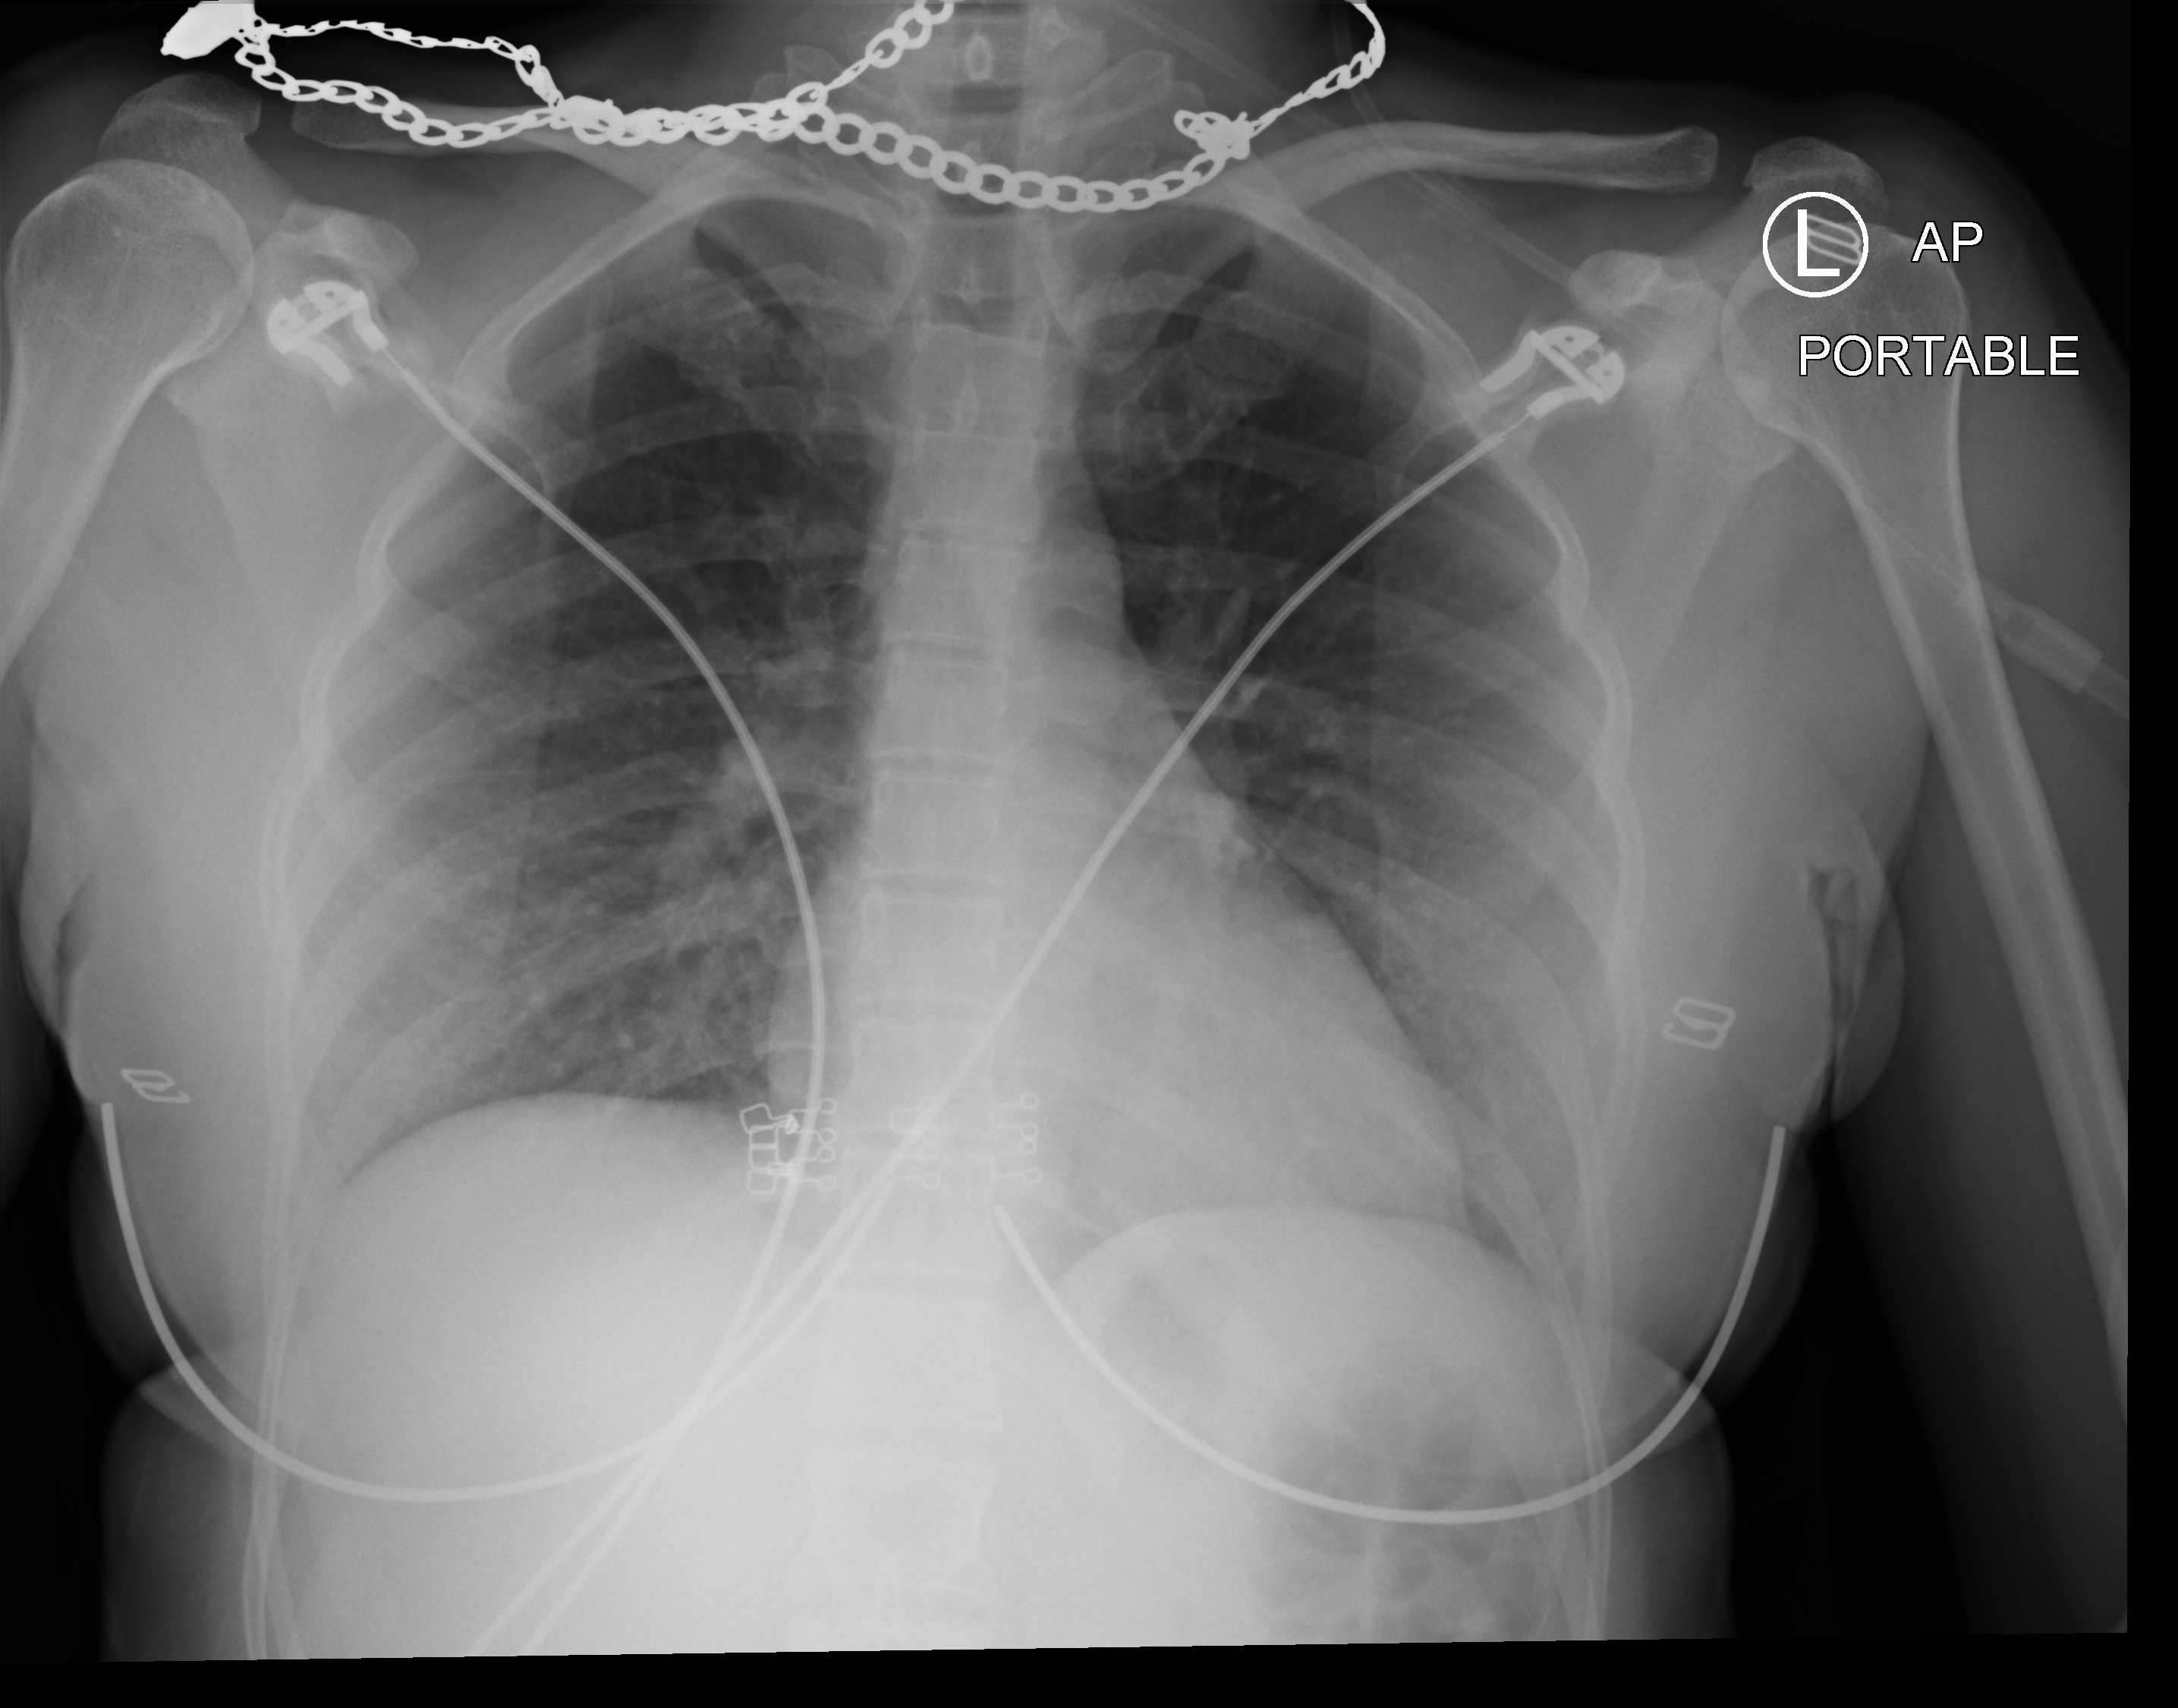
Bedside chest radiograph (computed radiography); anteroposterior (AP) projection. Female patient hospitalised with COVID-19, age 18–59 years.
From the hospital-stay record, not from the radiograph (when in the stay this image was taken is not recorded): smoking status (admission record): former; mechanically ventilated during this hospital stay: no; admitted to intensive care during this hospital stay: no.